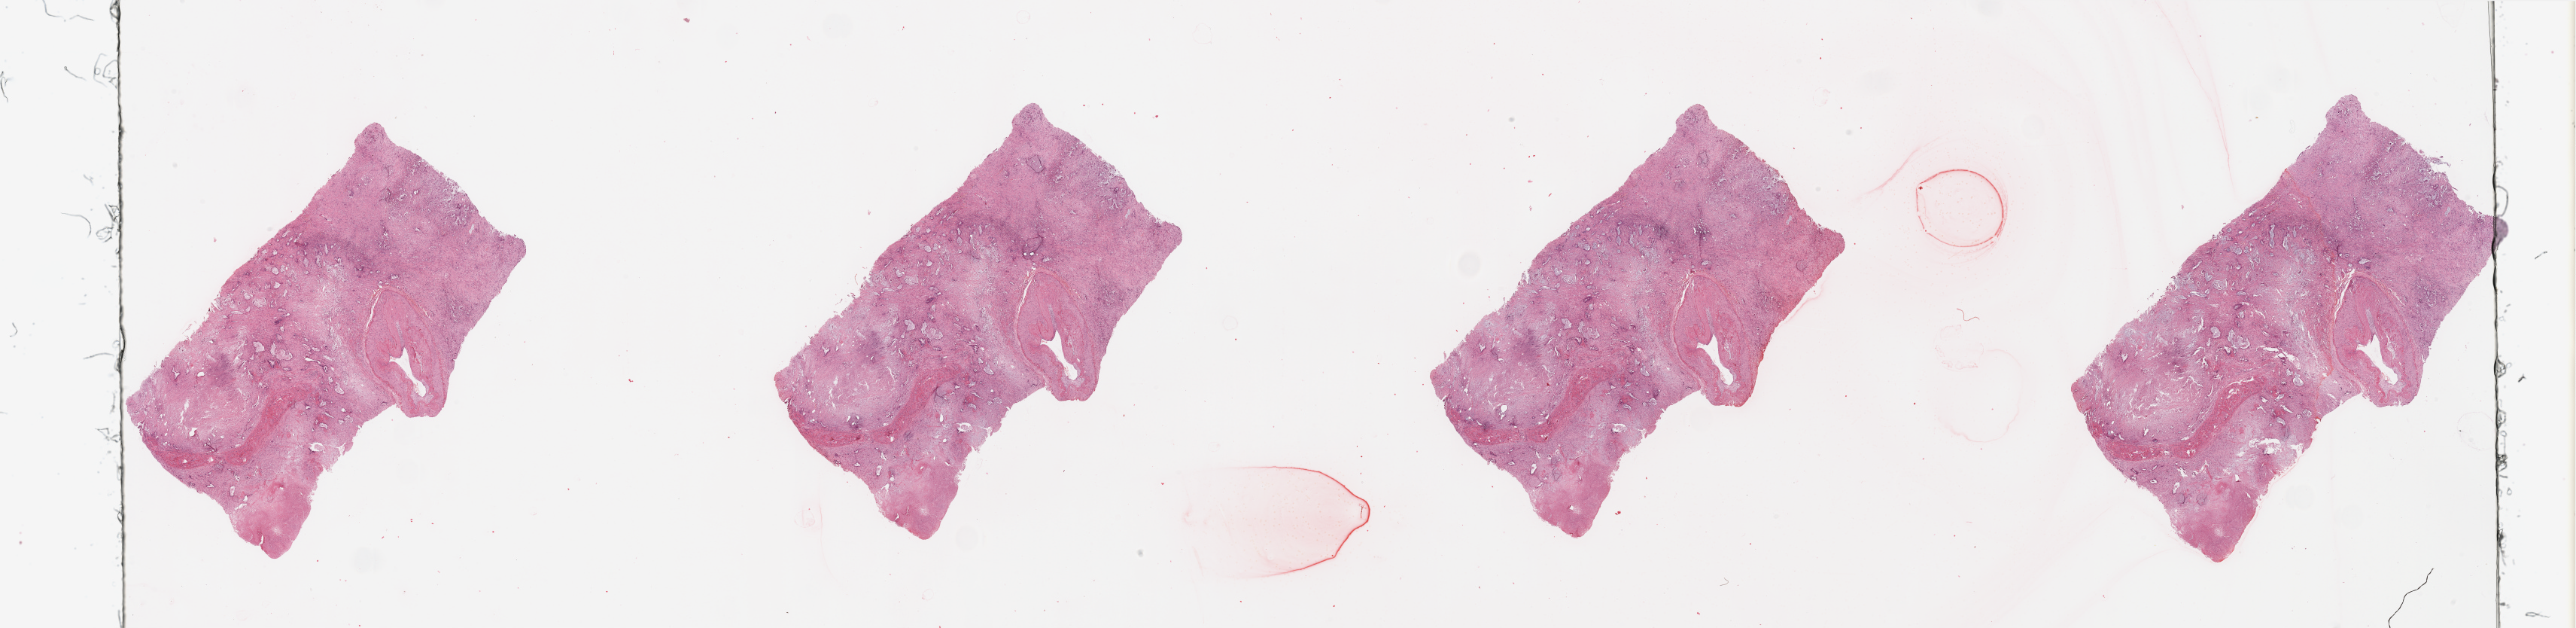
Whole-slide histology image, H&E — shown as a low-resolution overview of the whole scanned area (about 54.1 x 13.2 mm). Pancreas, tumour tissue. Male, 72 y/o. Histologic grade: G2 (moderately differentiated).
AJCC pathologic stage: IB. Diagnosis: Infiltrating duct carcinoma, NOS.